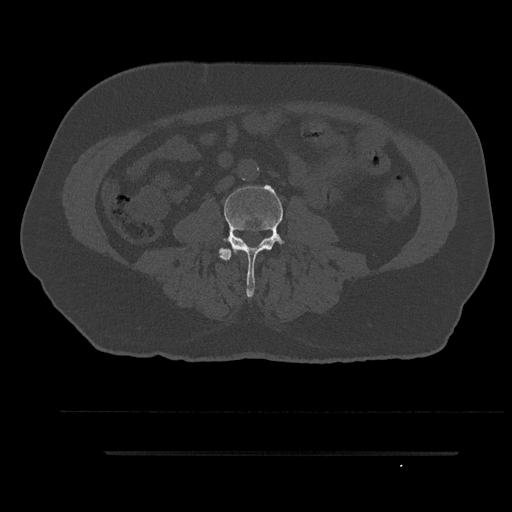
CT including the spine, one axial slice. Position 35 of 797 along the scan axis. Reconstruction kernel Br40s/3. 120 kVp. Bone window (W 1800 / L 400 HU). 0.5 mm slice thickness. 512 × 512 image matrix, field of view 432 × 432 mm. Patient: male, 63 years. From the clinical record (not read from this slice): primary cancer: renal.
Outlined on this slice (semi-automatically segmented with operator editing):
- L3 vertebra: box from (x=219, y=185) to (x=285, y=298) px